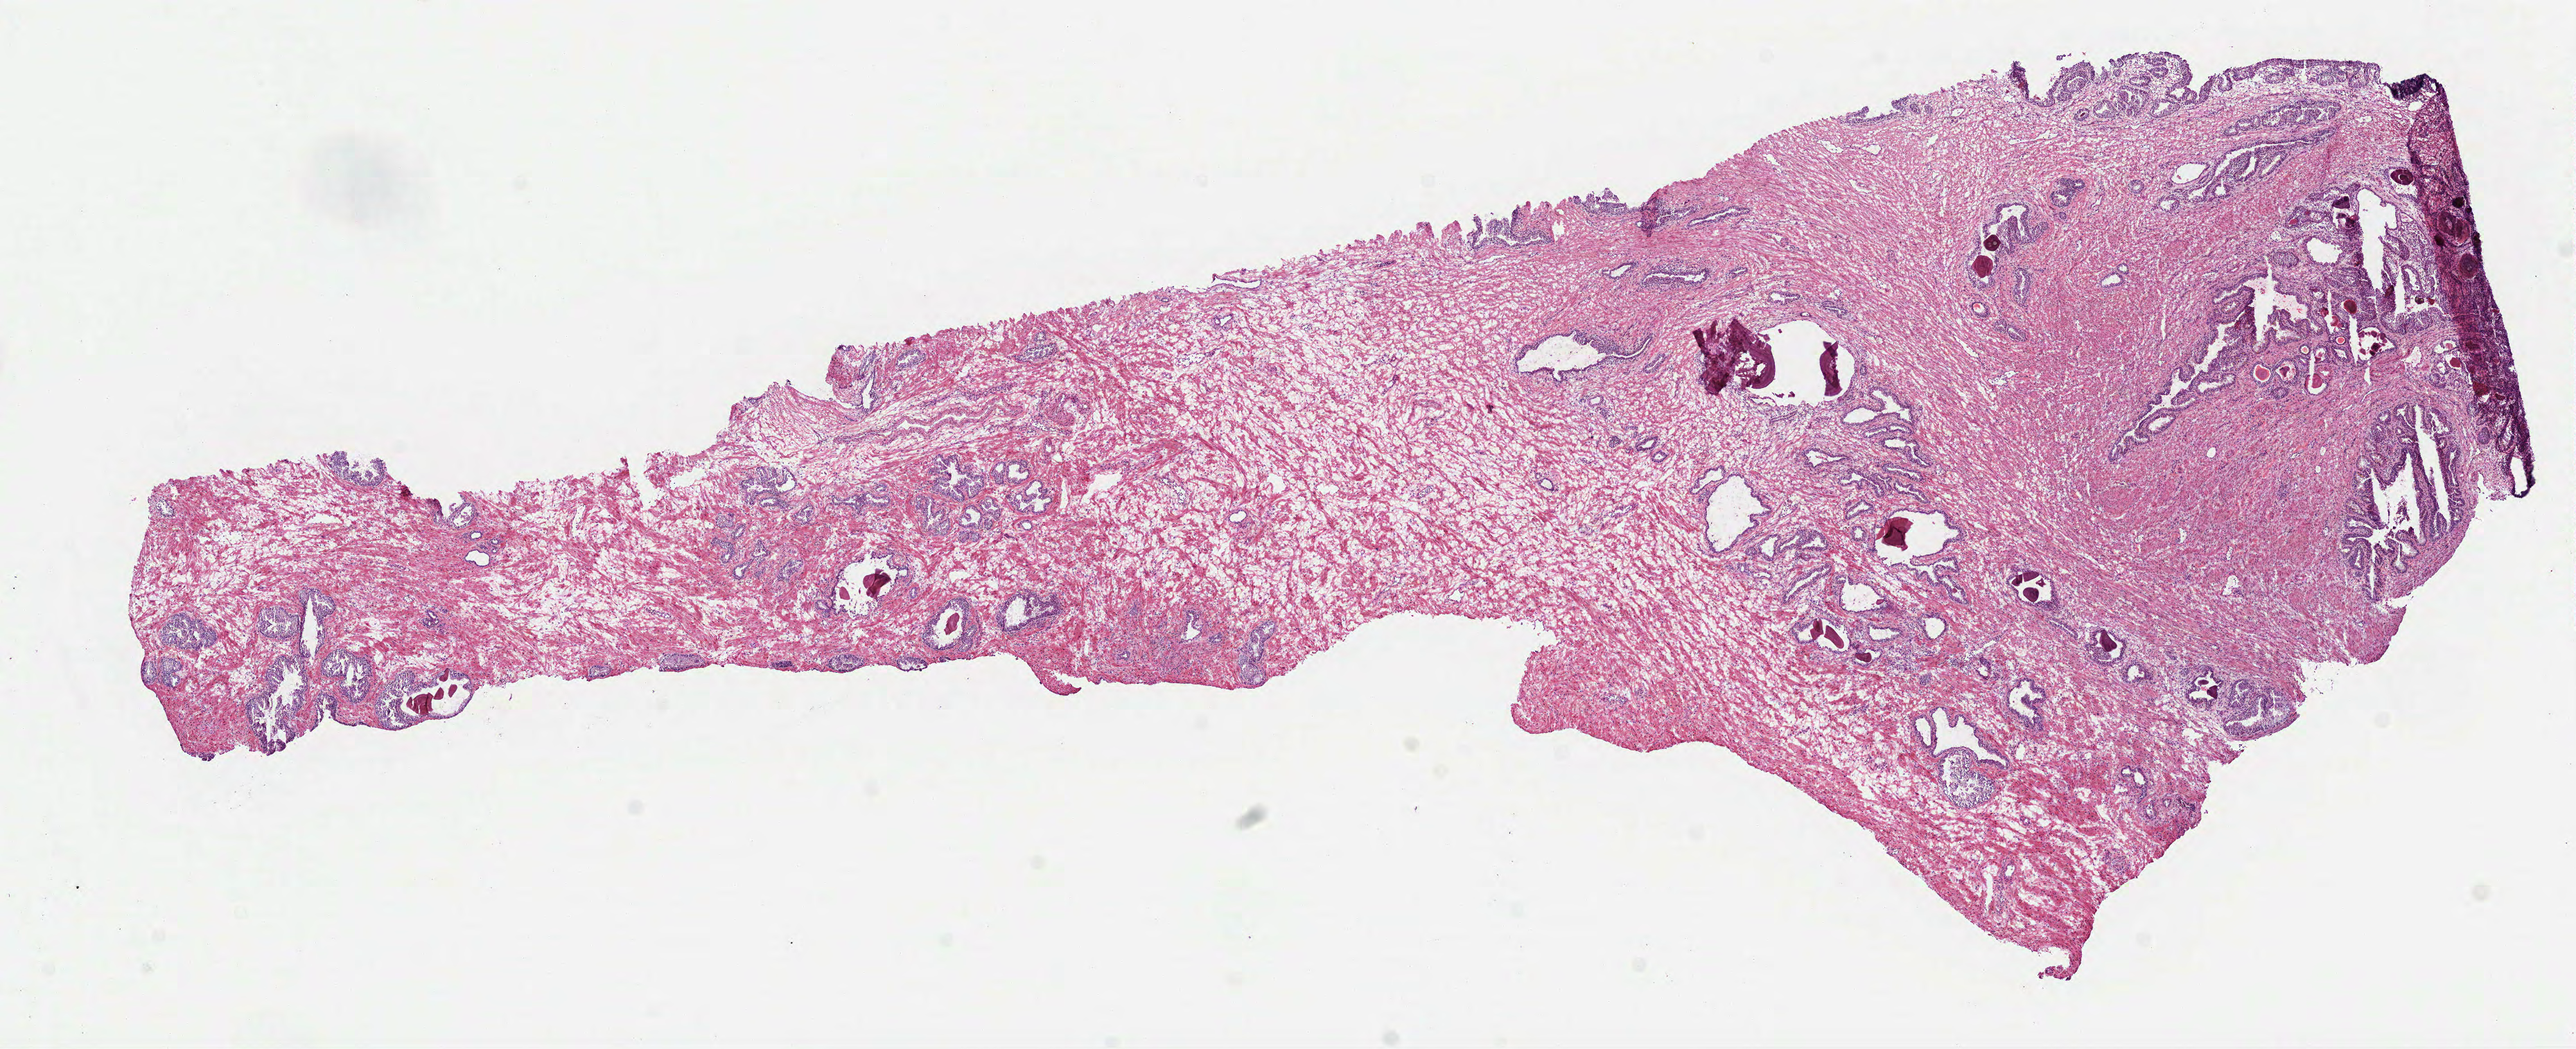
Digitized H&E-stained tissue section (whole slide), shown as a low-resolution overview of the whole scanned area (about 15.0 x 6.1 mm, acquisition: 40x scan). Frozen section. Sample: solid tissue normal (non-tumour tissue), prostate. Male patient; age at initial diagnosis 67 years.
This section: solid tissue normal sample (biorepository sample class). Patient diagnosis: Acinar cell carcinoma (prostate gland).